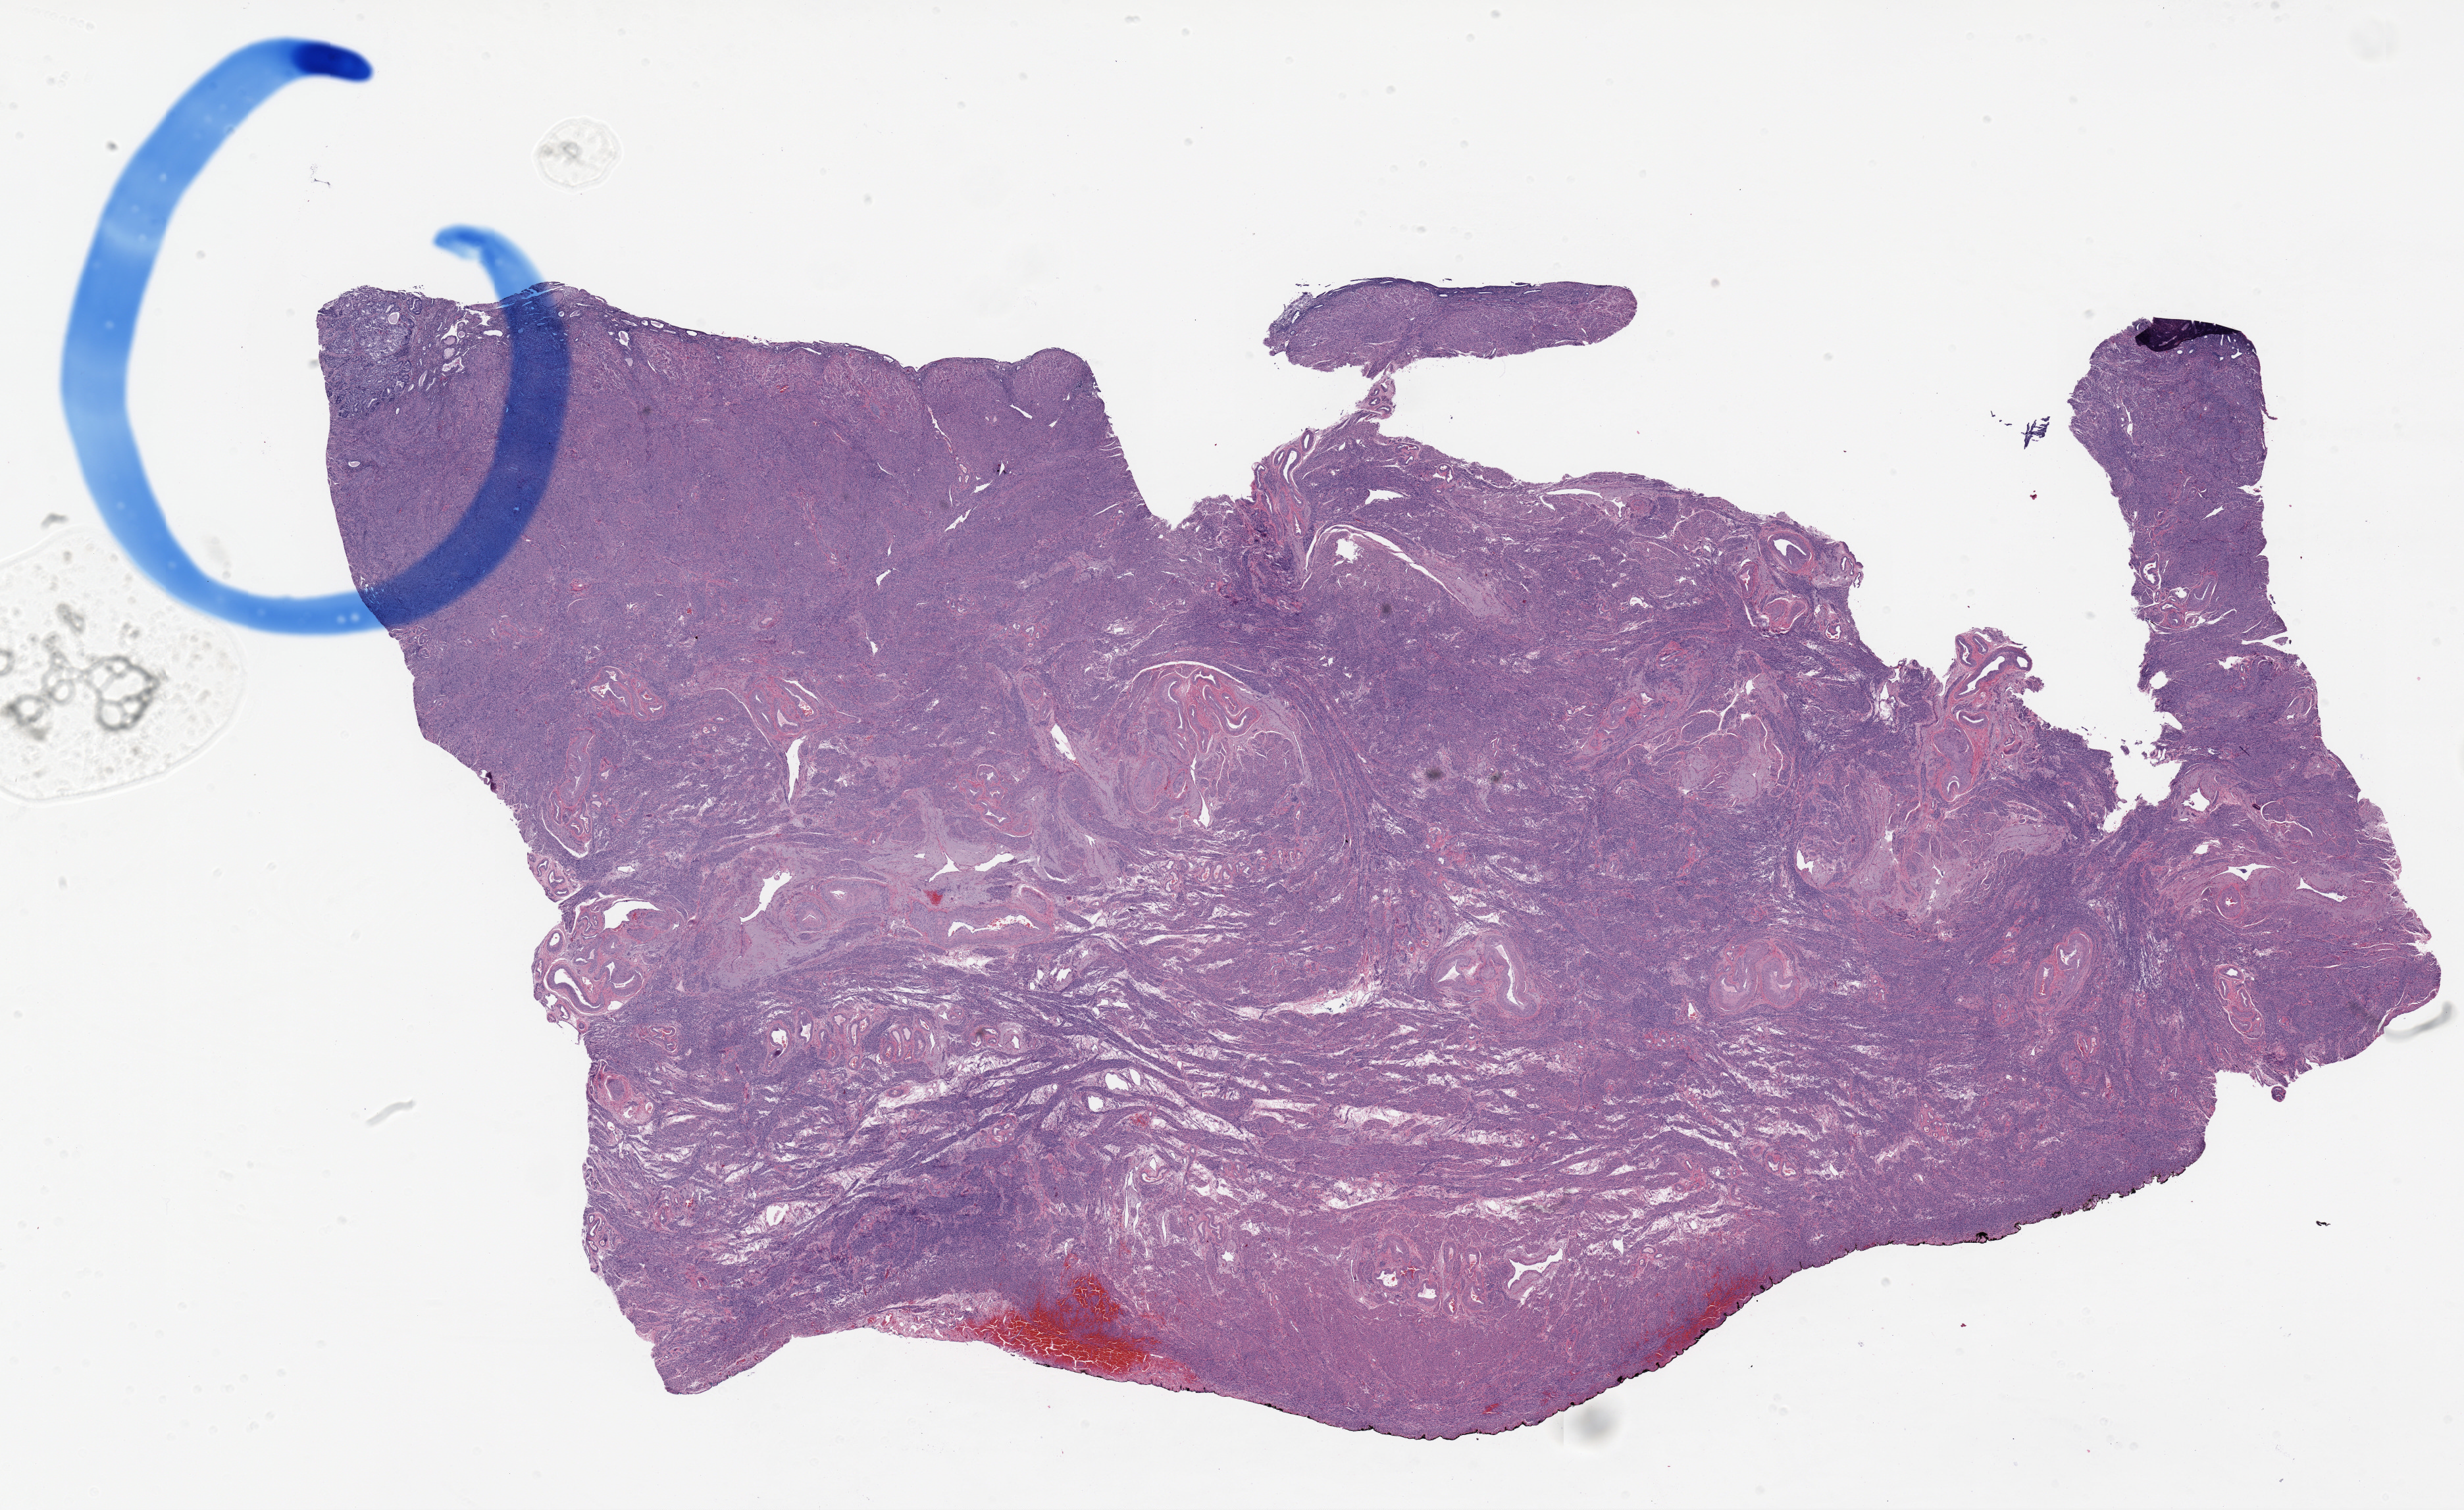
Whole-slide histology image, Hematoxylin and eosin (H&E) stained — low-resolution overview of the scanned area, about 29.8 x 18.3 mm (slide scanned at 20x), formalin-fixed paraffin-embedded (FFPE) diagnostic section, sample: primary tumour, uterus. Patient: female, age at initial diagnosis 54 years. Histologic grade: G3 (poorly differentiated).
* lymph nodes positive (case pathology): 0 of 2 examined
* FIGO stage: IA
* diagnosis: Endometrioid adenocarcinoma, NOS